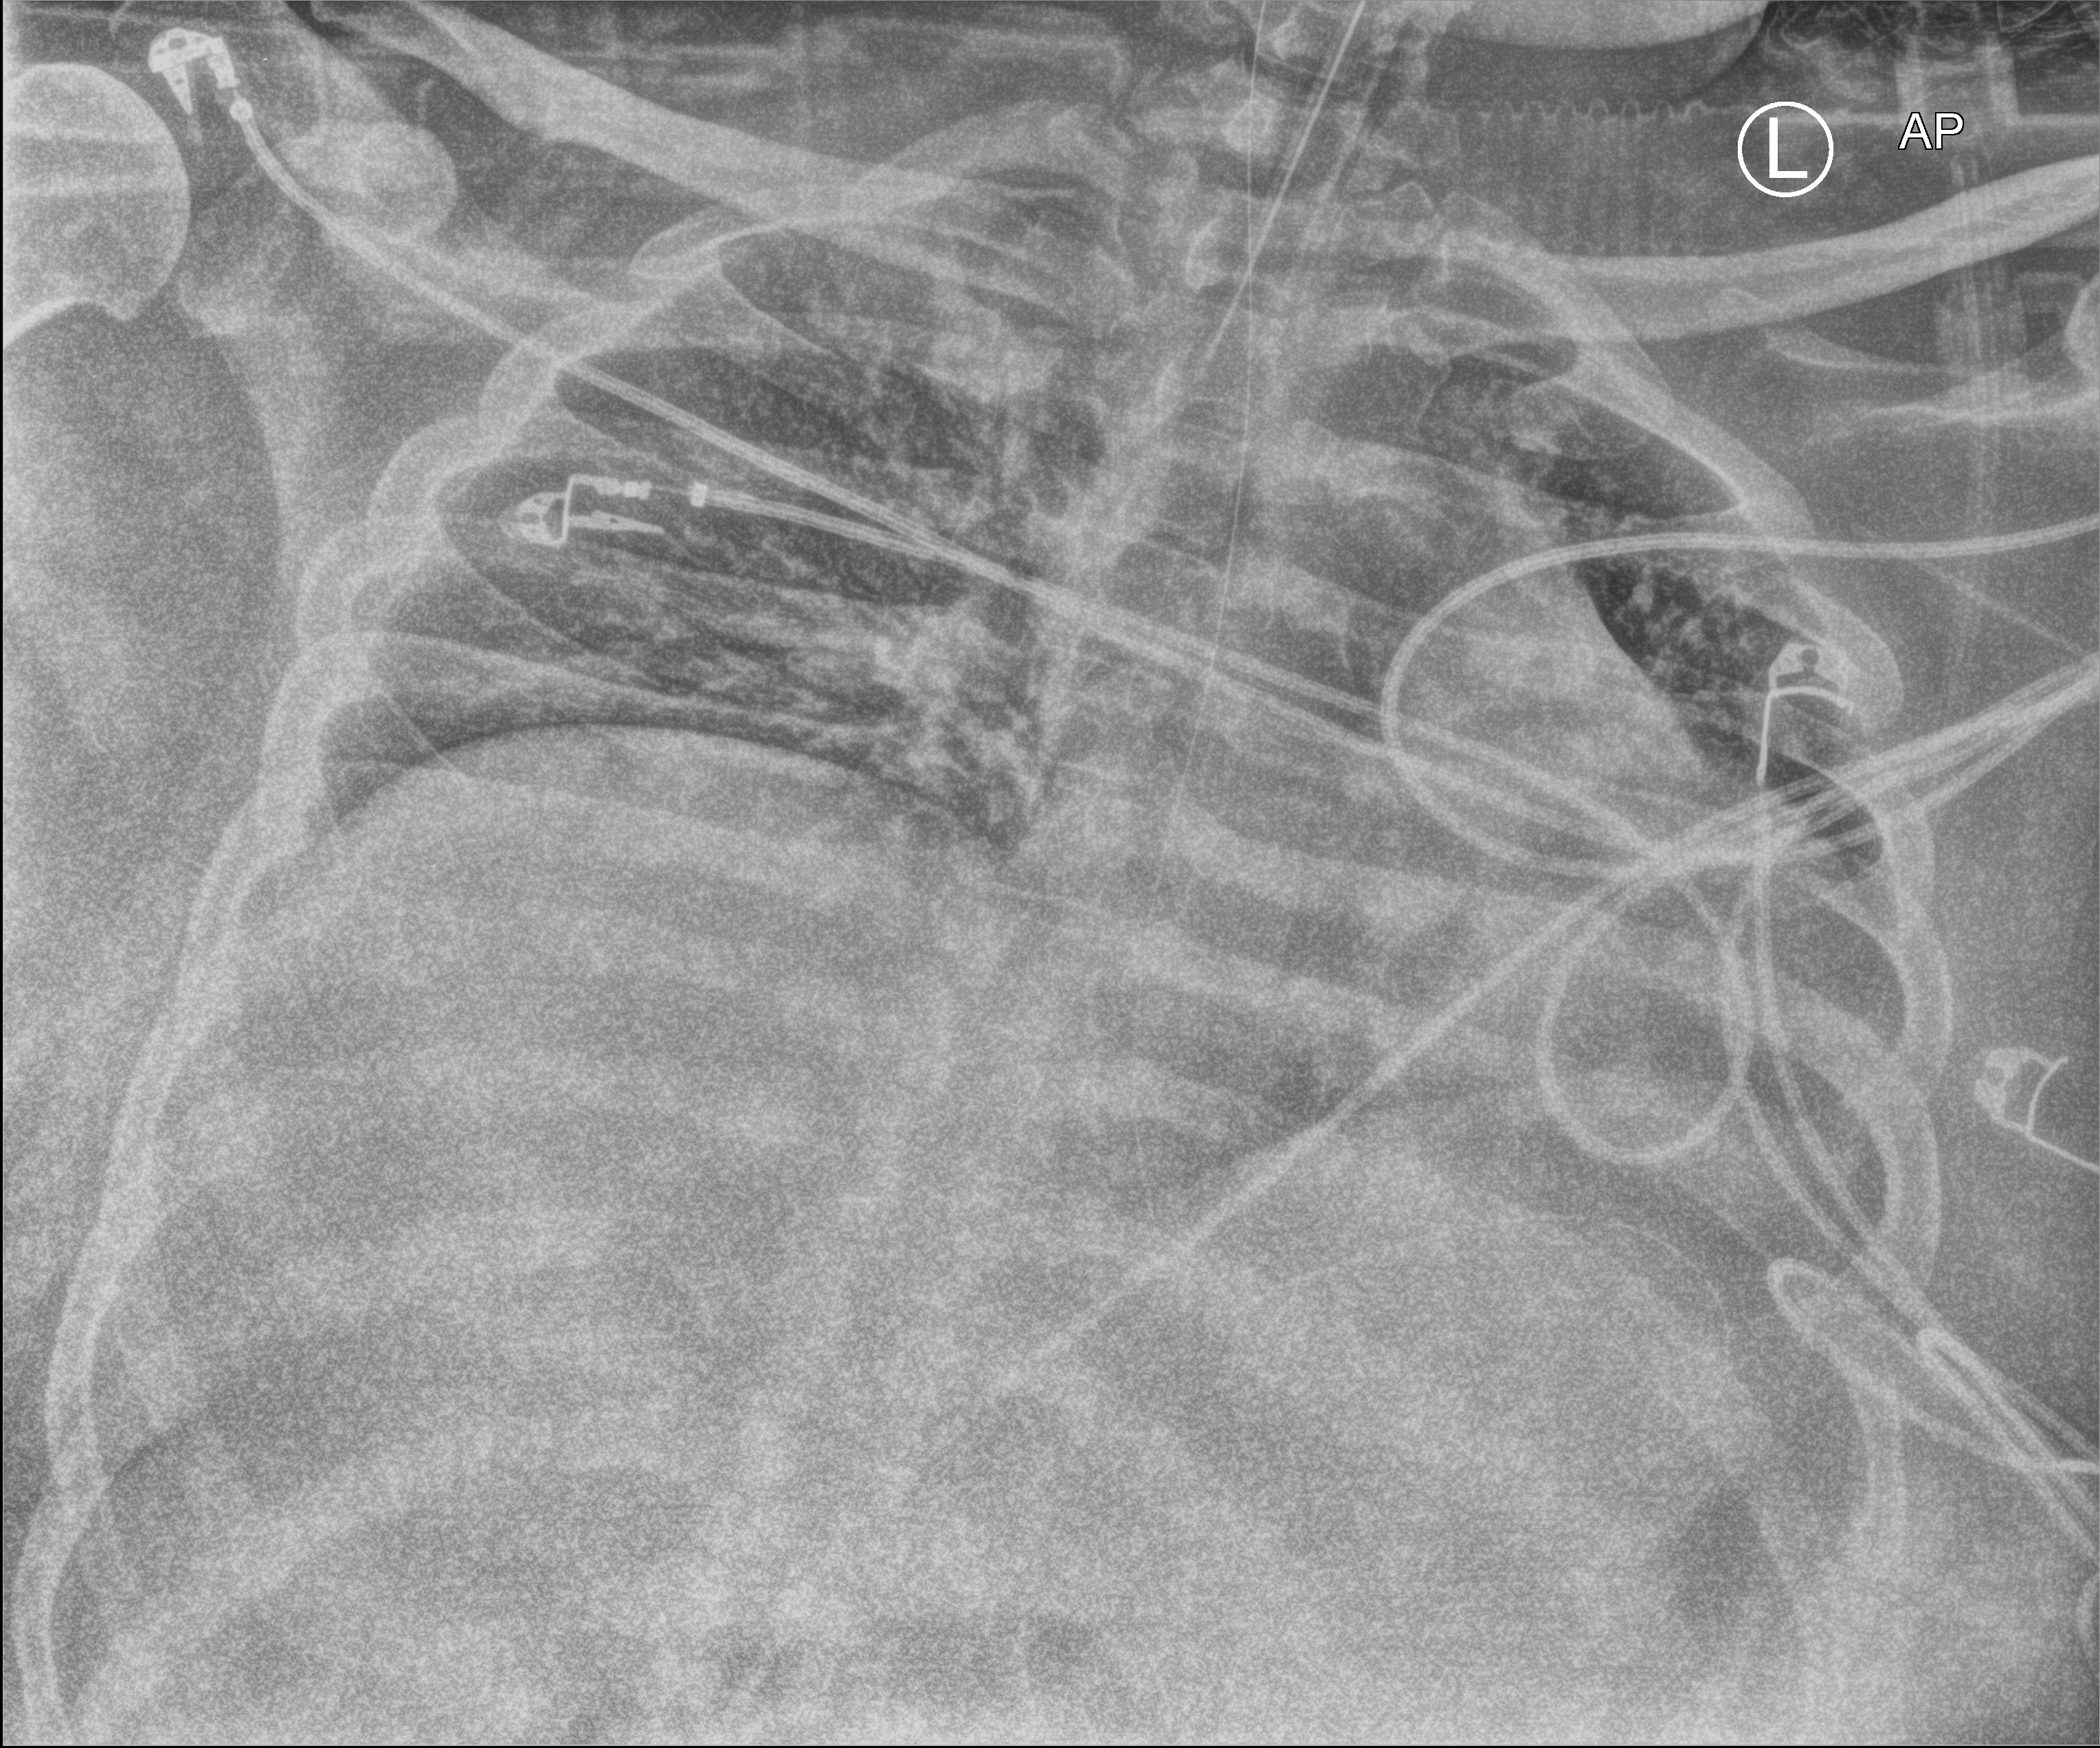
Bedside chest radiograph (computed radiography), anteroposterior (AP) projection. Patient hospitalised with COVID-19; male, aged 18–59 years.
Hospital-stay facts (about this admission, not read from this image; timing relative to this image not recorded):
- COPD (admission record): yes
- diabetes (admission record): yes
- length of hospital stay: 69 days